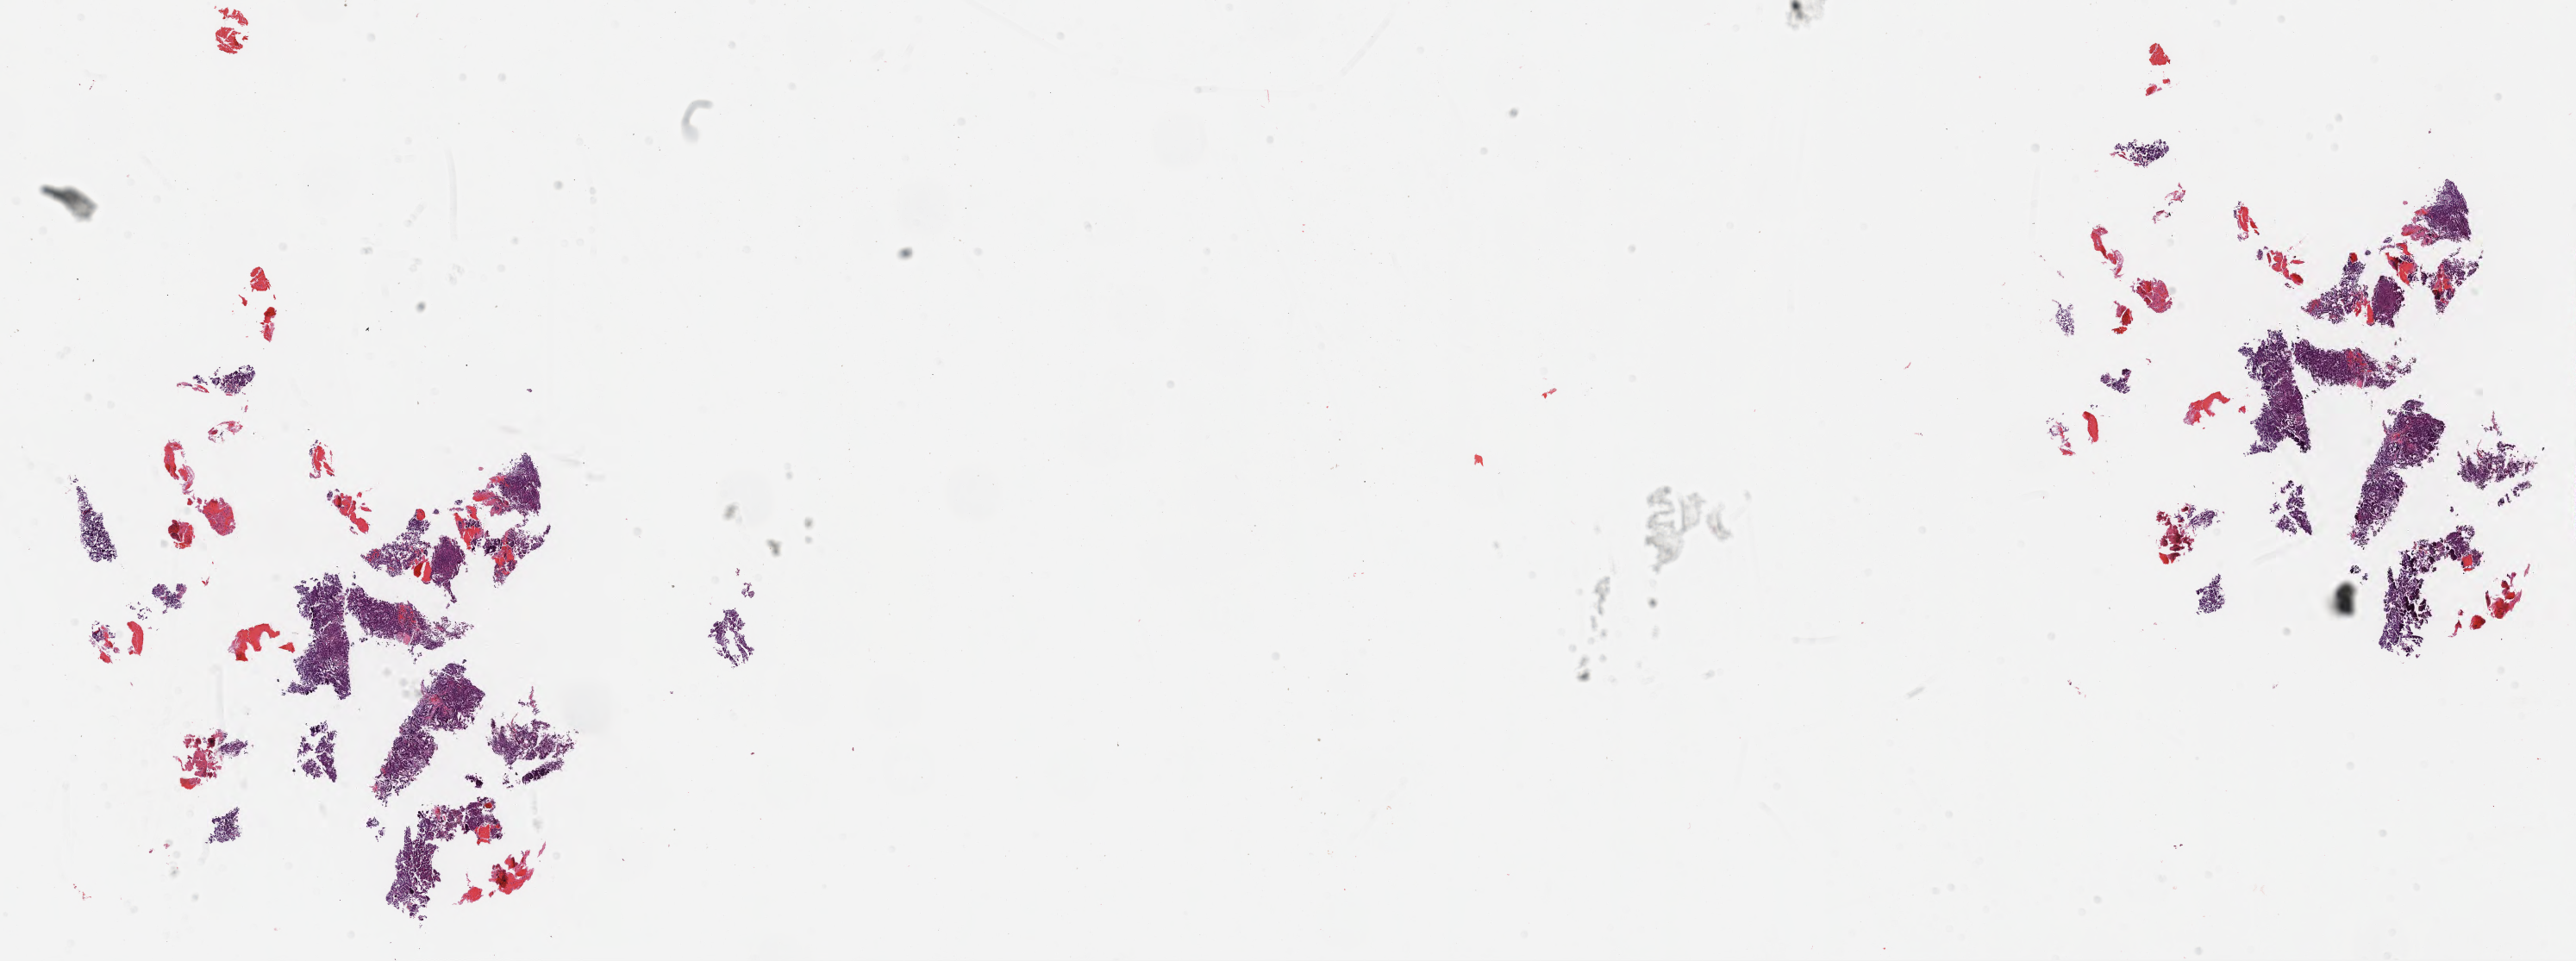
Digitized H&E tissue section (whole slide), whole scanned area (about 24.1 x 9.0 mm) shown as a low-resolution overview; FFPE section; sample: primary tumour, mesothelium. Patient: male, age at initial diagnosis 62 years.
* laterality: right
* AJCC pathologic stage: III
* diagnosis: Epithelioid mesothelioma, malignant (lung, NOS)